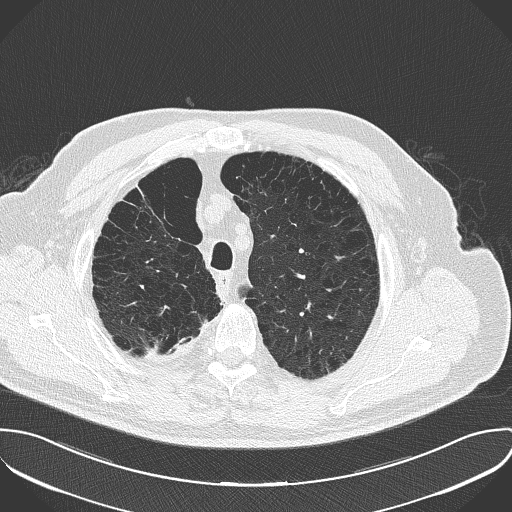
Axial slice from a low-dose chest CT screening exam. First (baseline) screen. Lung window (W 1500 / L -600 HU). 2 mm slice thickness. Lung (sharp) reconstruction kernel (B50f). Slice 38 of 181 in the series. 512 × 512 image matrix, field of view 388 × 388 mm. Male, age 68 years at enrolment. Current smoker at enrolment.
Lesion marked by an expert reader, bounding box <125,323,196,370> (left, top, right, bottom; pixels). The screening reader recorded 3 non-calcified nodules or masses ≥4 mm on this exam (left lower lobe, left upper lobe, right lower lobe); which of them this box marks is not recorded. Official screen result: positive, change unspecified: nodule(s) >= 4 mm or enlarging nodule(s), mass(es), or other non-specific abnormalities suspicious for lung cancer. Later outcome: lung cancer diagnosed 661 days after this screen — adenocarcinoma, NOS, right upper lobe, stage IV (AJCC 6th edition), 29 mm at pathology.